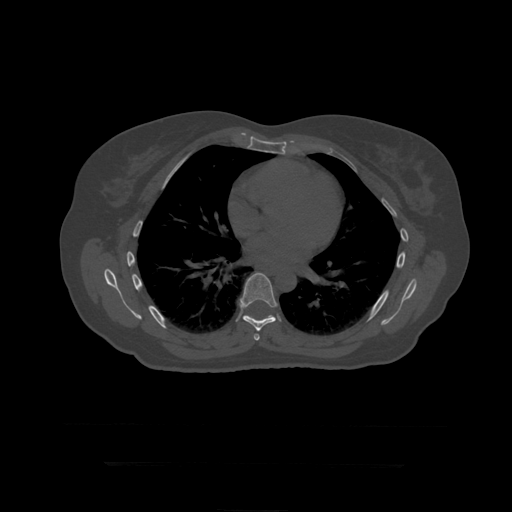
CT including the spine, one axial slice; 120 kVp; bone window (W 1800 / L 400 HU); 1.25 mm slice thickness; 512 × 512 image matrix, field of view 450 × 450 mm. Patient age 41 years. From the clinical record (not read from this slice): primary cancer: breast.
Structures marked on this image (semi-automatic segmentation, software-assisted and operator-edited):
- T7 vertebra: box from (x=254, y=334) to (x=260, y=341) px
- T8 vertebra: (x=240, y=273)–(x=277, y=332)
- T9 vertebra: (x=245, y=315)–(x=252, y=318)